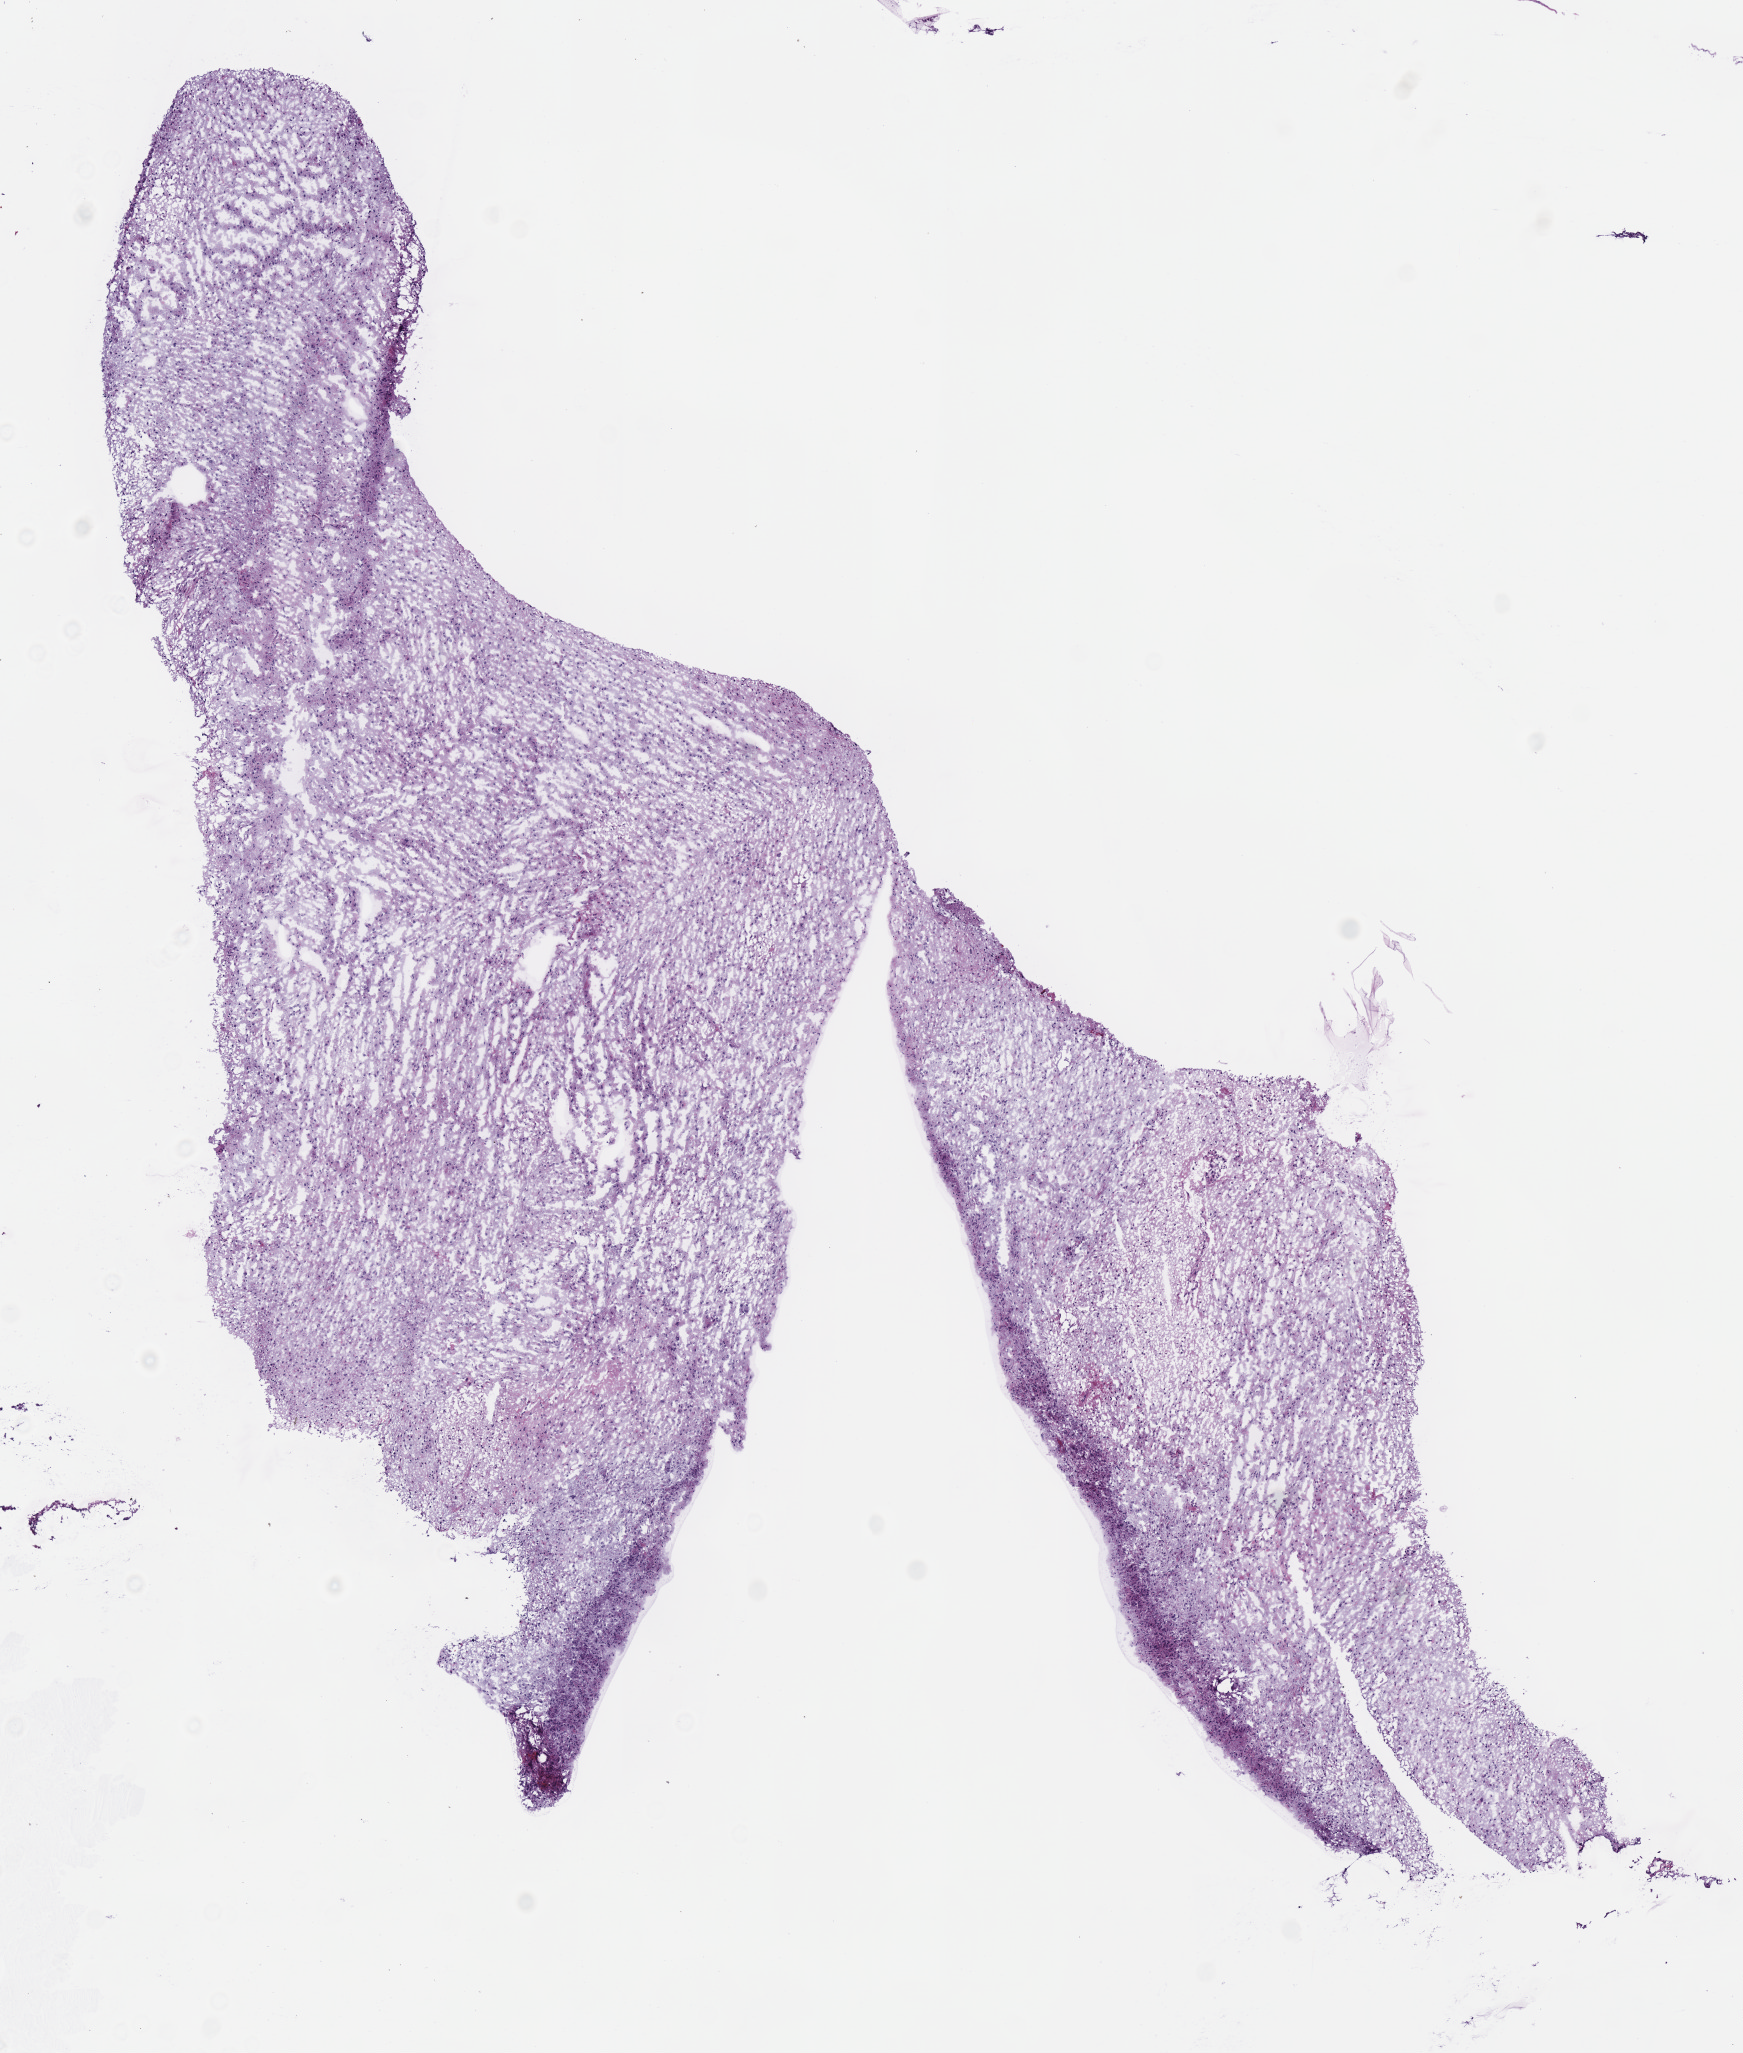
Whole-slide histology image, Hematoxylin and eosin (H&E) stained, whole scanned area (about 6.9 x 8.1 mm, acquisition: 40x scan) shown as a low-resolution overview, frozen section from the top of the tissue portion, primary tumour sample from the brain. Male patient; age at initial diagnosis 26 years. Histologic grade: G2 (moderately differentiated). Slide review estimates, as recorded: tumour cells 100%, tumour nuclei 65%, normal cells 0%, stromal cells 0%, necrosis 0%.
Histologic diagnosis: Oligodendroglioma, NOS (cerebrum).